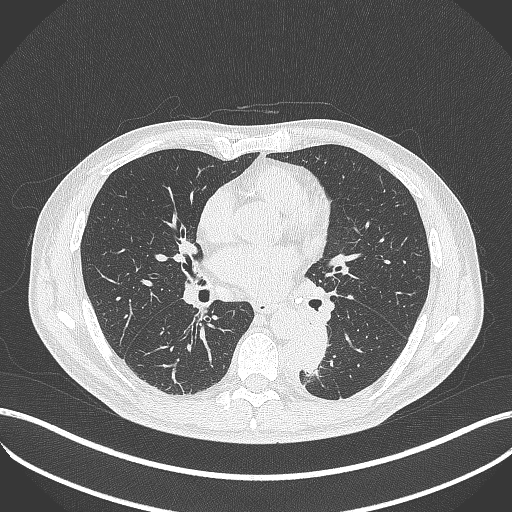
Chest CT, one axial slice. Slice 204 of 451 in the series (ordered by position). Lung window (W 1500 / L -600 HU). 1 mm slice thickness. 512 × 512 image matrix, field of view 400 × 400 mm. Patient: male, 72 years. From the clinical record (not read from this slice): clinical TNM (as recorded): T2b N0 M1.
Annotated regions visible in this slice (bounding box drawn by a radiologist):
- lung tumour (recorded histology: adenocarcinoma): bounding box [x1, y1, x2, y2] px = [284, 321, 333, 383]